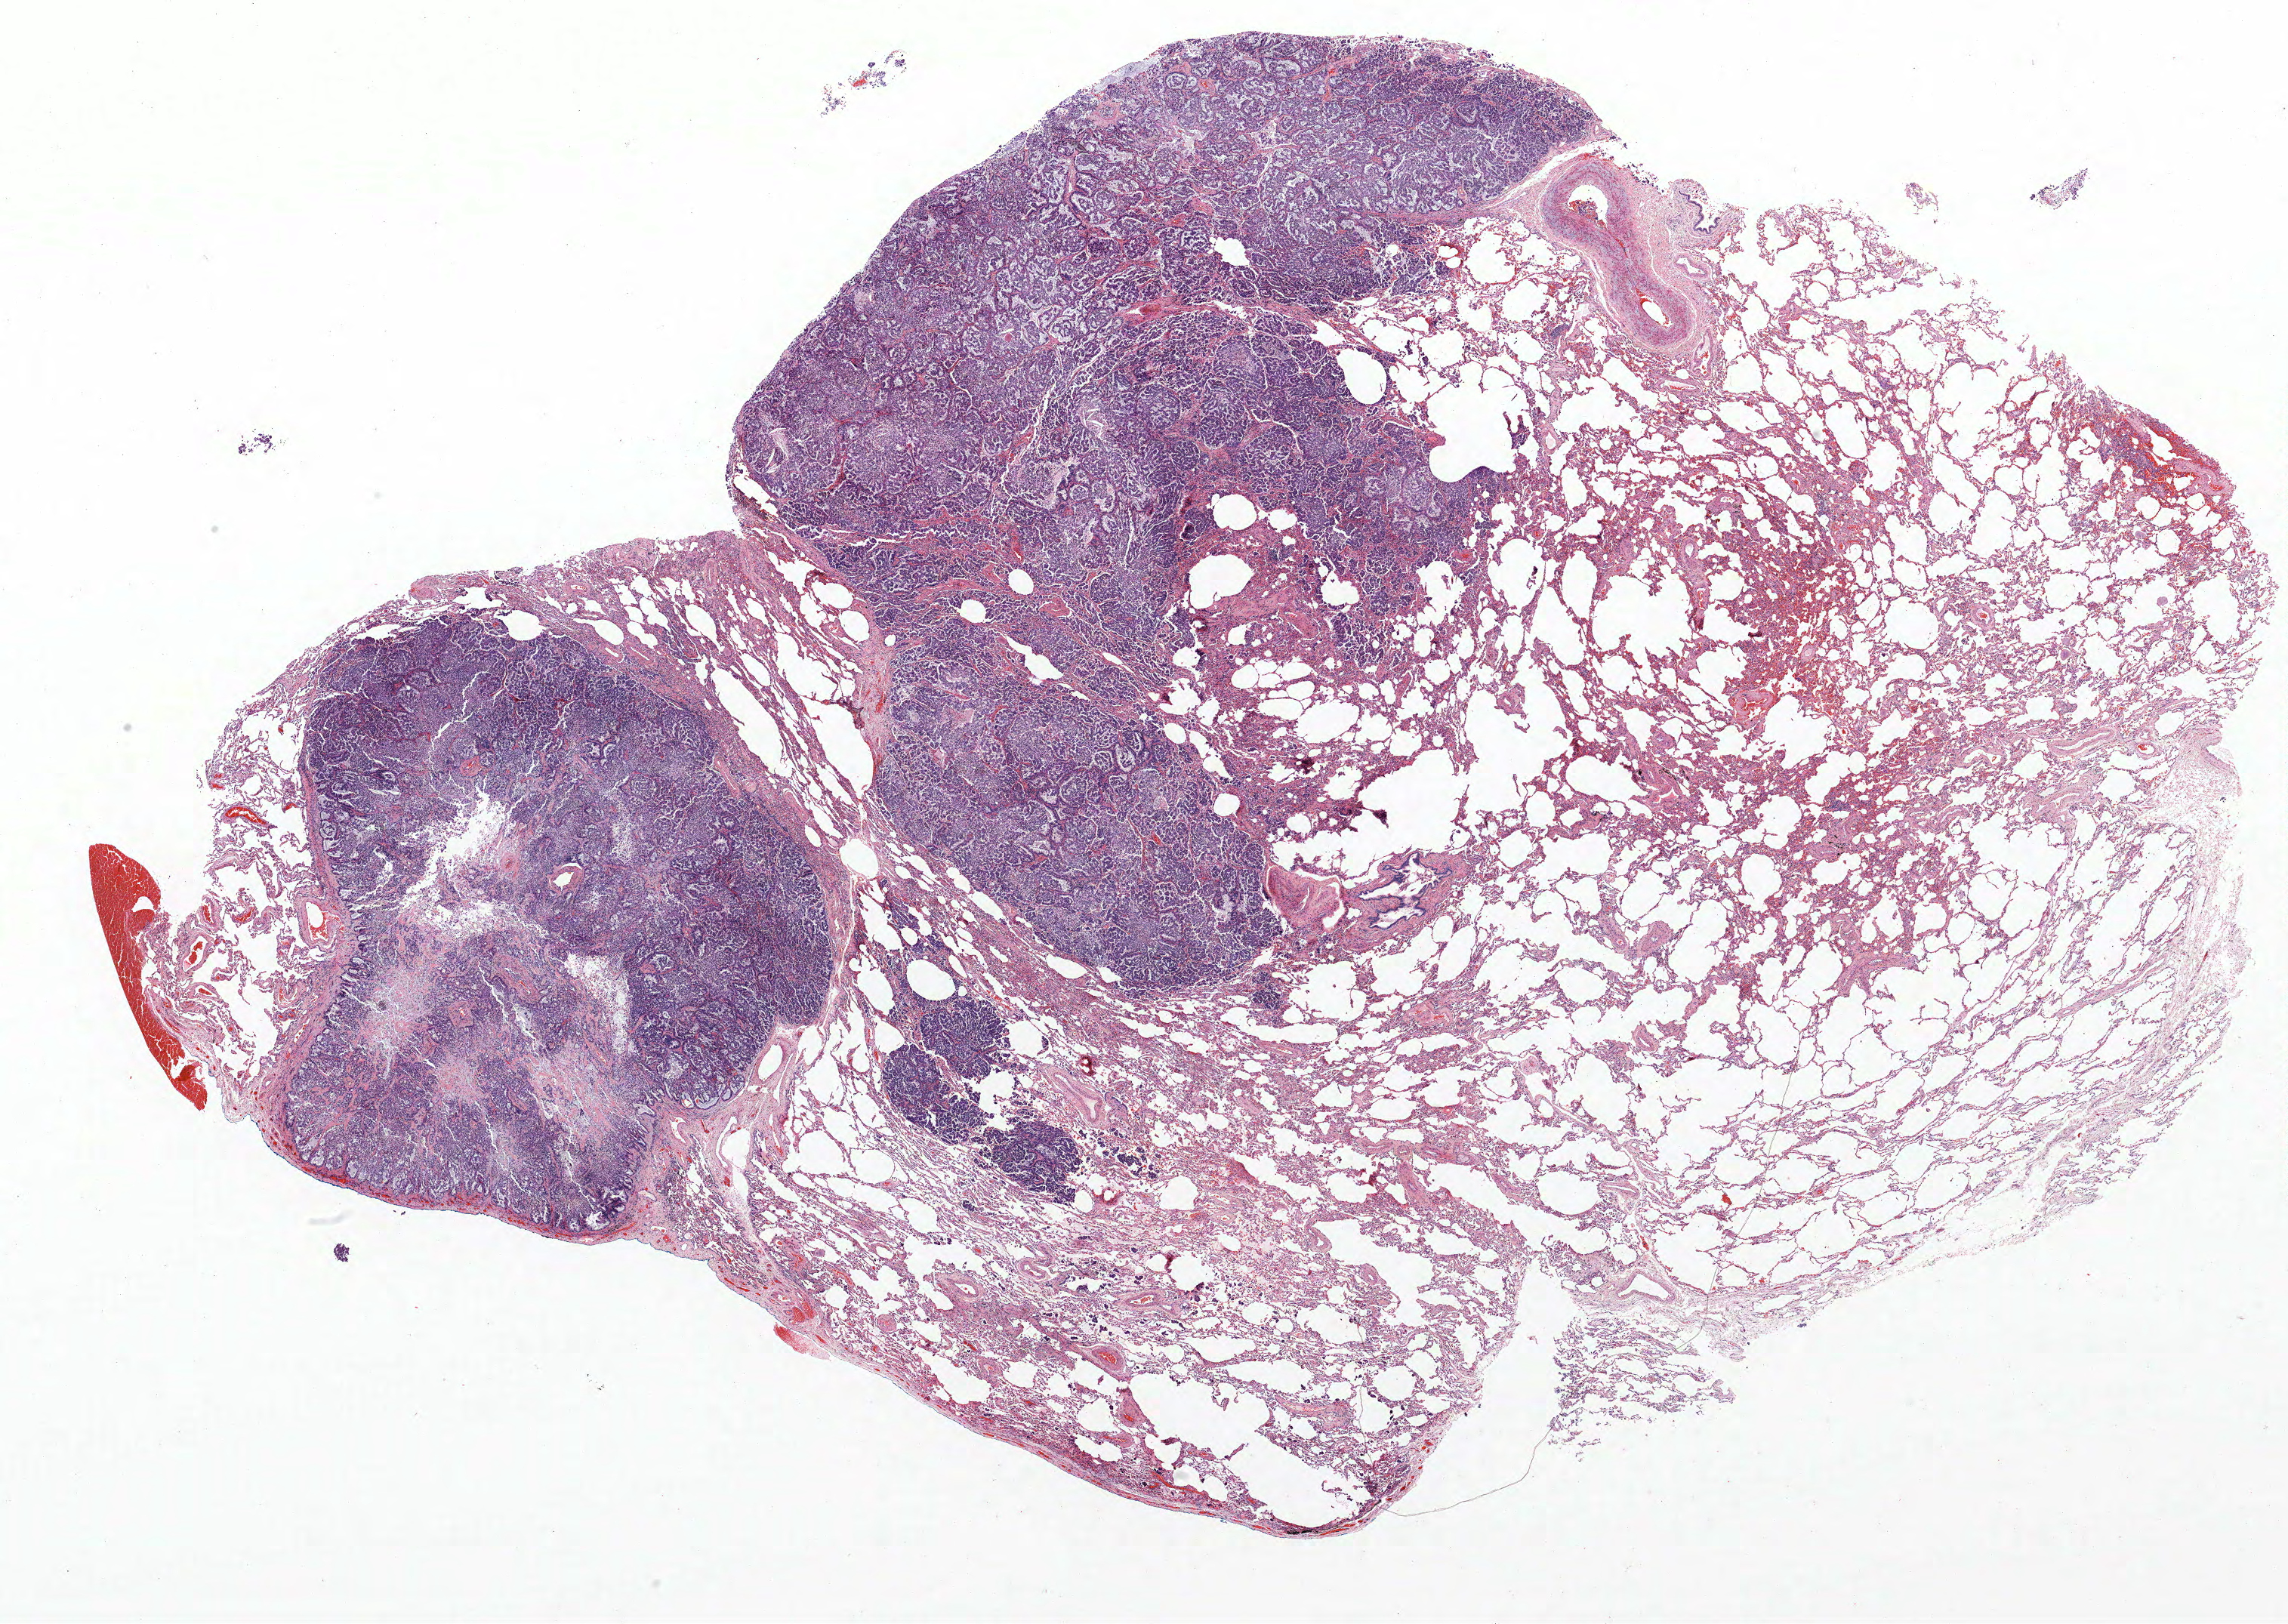
Whole-slide histology image, H&E — low-resolution overview of the scanned area, about 24.2 x 17.2 mm (slide scanned at 40x), FFPE section, lung. Male, age 74 at enrolment. Former smoker at enrolment. Grade: well differentiated (G1).
Primary tumour location (clinical record): right middle lobe. Tumour size (pathology): 20 mm. Participant's lung-cancer diagnosis: Papillary adenocarcinoma, NOS. Stage (AJCC 6th edition): IA. ICD-O-3 topography: middle lobe of lung (C34.2).